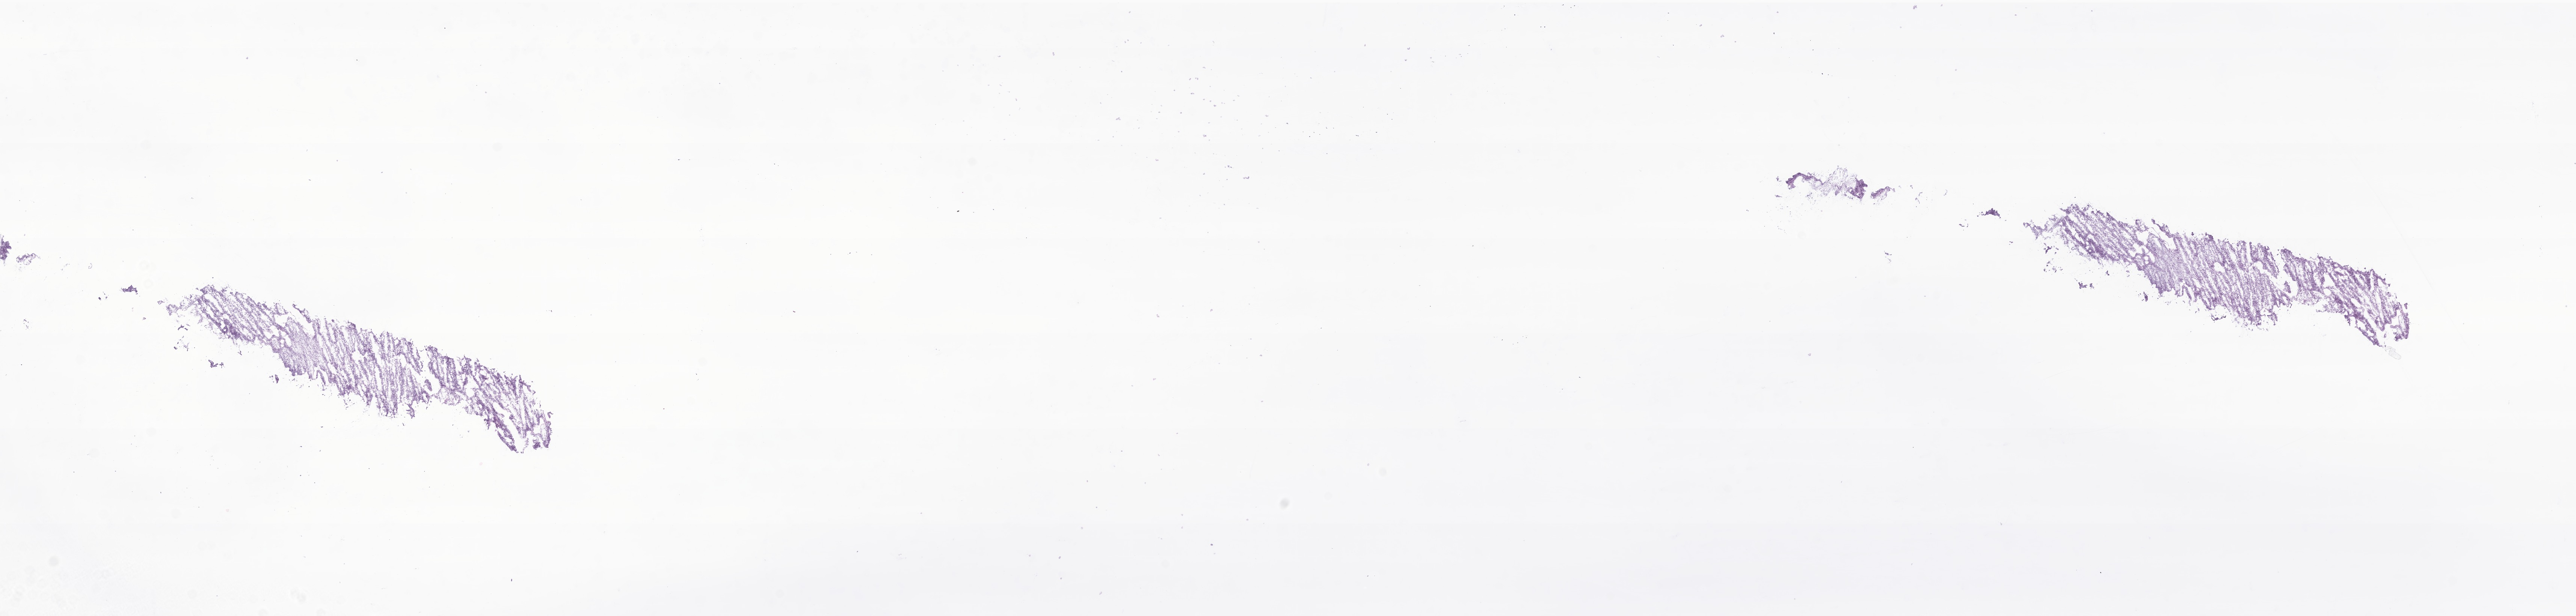
Whole-slide image, H&E stain of tumor tissue from the soft tissue, shown as a low-resolution overview of the whole scanned area (about 28.9 x 6.9 mm); frozen section (OCT-embedded). Male patient, age 693 days (about 1.9 years).
Diagnosis: Embryonal rhabdomyosarcoma, NOS.